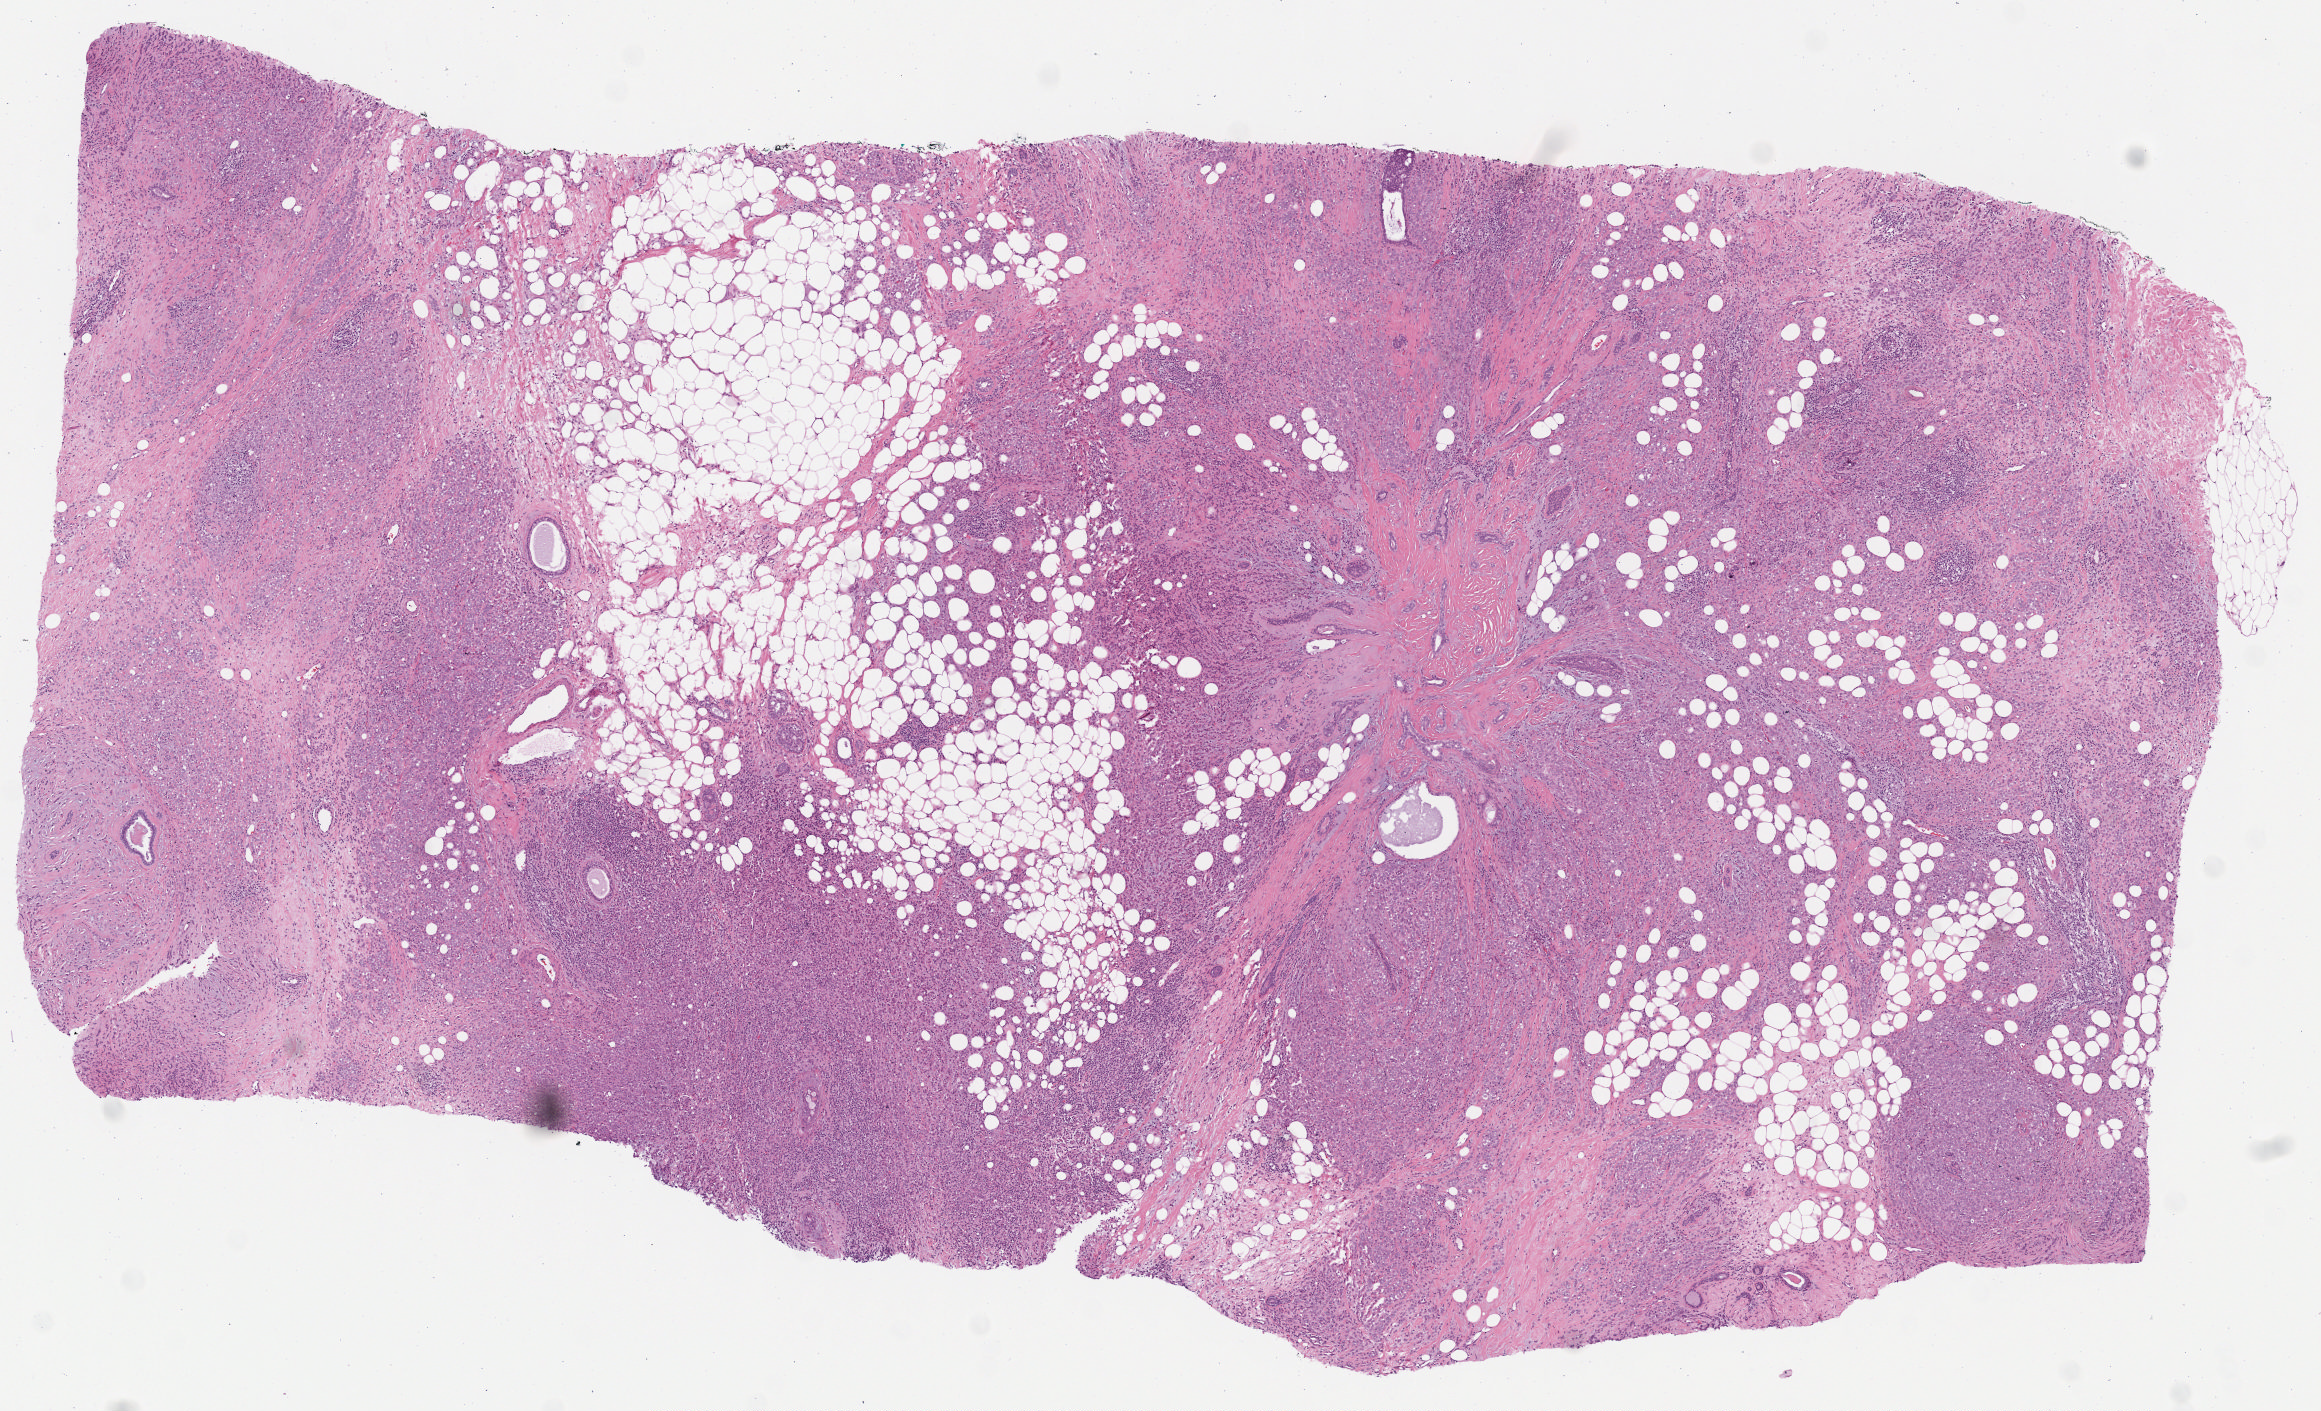
Digitized H&E tissue section (whole slide) — low-resolution overview of the scanned area, about 9.4 x 5.7 mm (slide scanned at 40x); formalin-fixed paraffin-embedded (FFPE) diagnostic section; primary tumour sample from the breast. Female, age 68 years at initial diagnosis.
- TNM: T2 N1mi MX
- laterality: left
- AJCC pathologic stage: IIB (7th edition)
- lymph nodes positive (case pathology): 1 of 3 examined
- histologic diagnosis: Lobular carcinoma, NOS